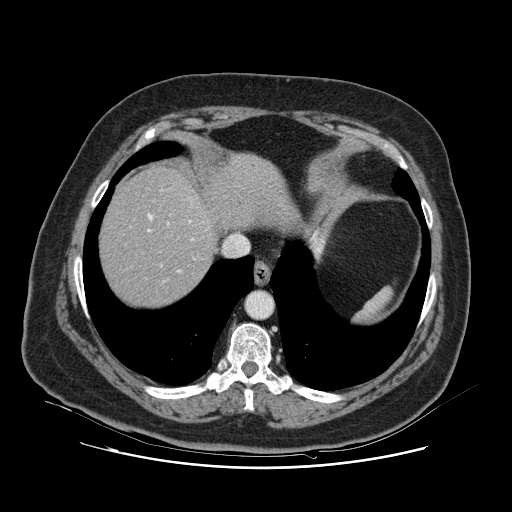
Contrast-enhanced abdominal CT, one axial slice. Slice 105 of 132 in the series (ordered by position). 120 kVp. Intravenous contrast given. Soft-tissue window (W 400 / L 40 HU). 2.5 mm slice thickness. 512 × 512 image matrix, field of view 391 × 391 mm. Female patient, age 73 years. Case-level facts recorded for this patient, not image findings: diagnosis: colorectal cancer liver metastases, imaged before liver resection; multiple liver metastases: no; largest metastasis: 7 cm; disease in both lobes: no.
Annotated regions visible in this slice (manually delineated by an expert):
- hepatic veins: box from (x=131, y=214) to (x=194, y=272) px
- liver: (x=101, y=169)–(x=278, y=306)
- planned liver remnant (the part of the liver to remain after resection): (x=102, y=169)–(x=217, y=306)
- portal vein (with intrahepatic branches): (x=161, y=222)–(x=169, y=266)